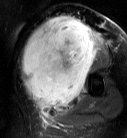
MRI of an extremity soft-tissue mass, one axial slice. T2-weighted fat-saturated. MR volume resampled by the dataset authors to the PET/CT grid (not the native acquisition matrix). 3.27 mm slice thickness. 127 × 138 image matrix, field of view 124 × 135 mm. Female patient. Case-level facts recorded for this patient, not image findings: histological type: pleiomorphic leiomyosarcoma; grade: high; site of the primary tumour: left biceps.
Annotated regions visible in this slice (expert contour drawn on MRI and transferred to this co-registered scan by the dataset authors):
- gross tumour volume including surrounding oedema: box from (x=20, y=16) to (x=103, y=113) px
- gross tumour volume (mass): (x=20, y=16)–(x=96, y=108)